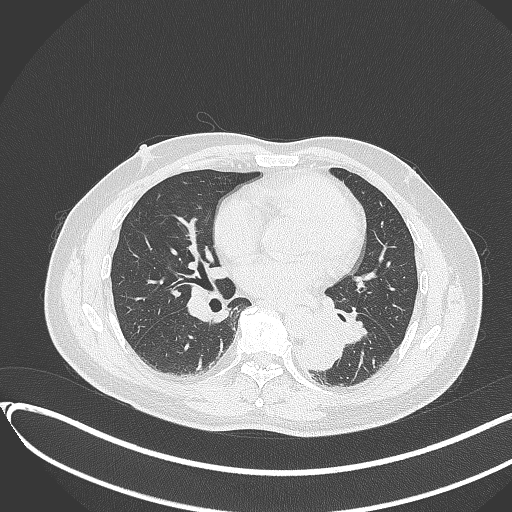
Chest CT, one axial slice. Position 158 of 417 along the scan axis. 120 kVp. Lung window (W 1500 / L -600 HU). 1 mm slice thickness. 512 × 512 image matrix, field of view 400 × 400 mm. Male patient, age 54 years. Case-level facts recorded for this patient, not image findings: clinical TNM (as recorded): T3 N0 M0.
Outlined on this slice (bounding box drawn by a radiologist):
- lung tumour (recorded histology: squamous cell carcinoma): bounding box (x1, y1, x2, y2) in pixels: (298, 328, 345, 372)